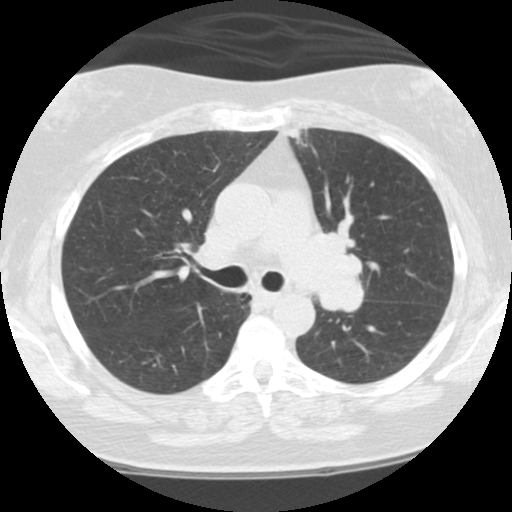
Low-dose screening chest CT, one axial slice; position 70 of 108 along the scan axis; lung window (W 1500 / L -600 HU); 2.5 mm slice thickness; 512 × 512 image matrix, field of view 300 × 300 mm.
Annotated regions visible in this slice (expert manual segmentation):
- lesion 1 (tumor, hilum of left lung): bounding box [x1, y1, x2, y2] px = [292, 233, 364, 312]